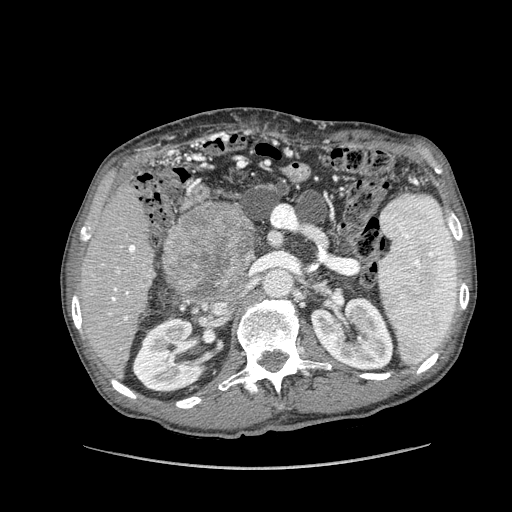
Contrast-enhanced abdominal CT (liver protocol), one axial slice; slice 55 of 162 in the series (ordered by position); 100 kVp; soft-tissue window (W 400 / L 40 HU); 2.5 mm slice thickness; 512 × 512 image matrix, field of view 400 × 400 mm. Case-level facts recorded for this patient, not image findings: diagnosis: hepatocellular carcinoma (patient treated with transarterial chemoembolisation; whether this scan precedes or follows treatment is not stated here); TNM stage (as recorded): Stage-IIIA.
Outlined on this slice (semi-automatically segmented with operator editing):
- liver parenchyma outside the tumour (the mass and vessels are separate outlines, so this box may not span the whole liver): bounding box <80,184,154,375> (left, top, right, bottom; pixels)
- mass: <164,204,255,298>
- liver vessels: <112,245,135,321>